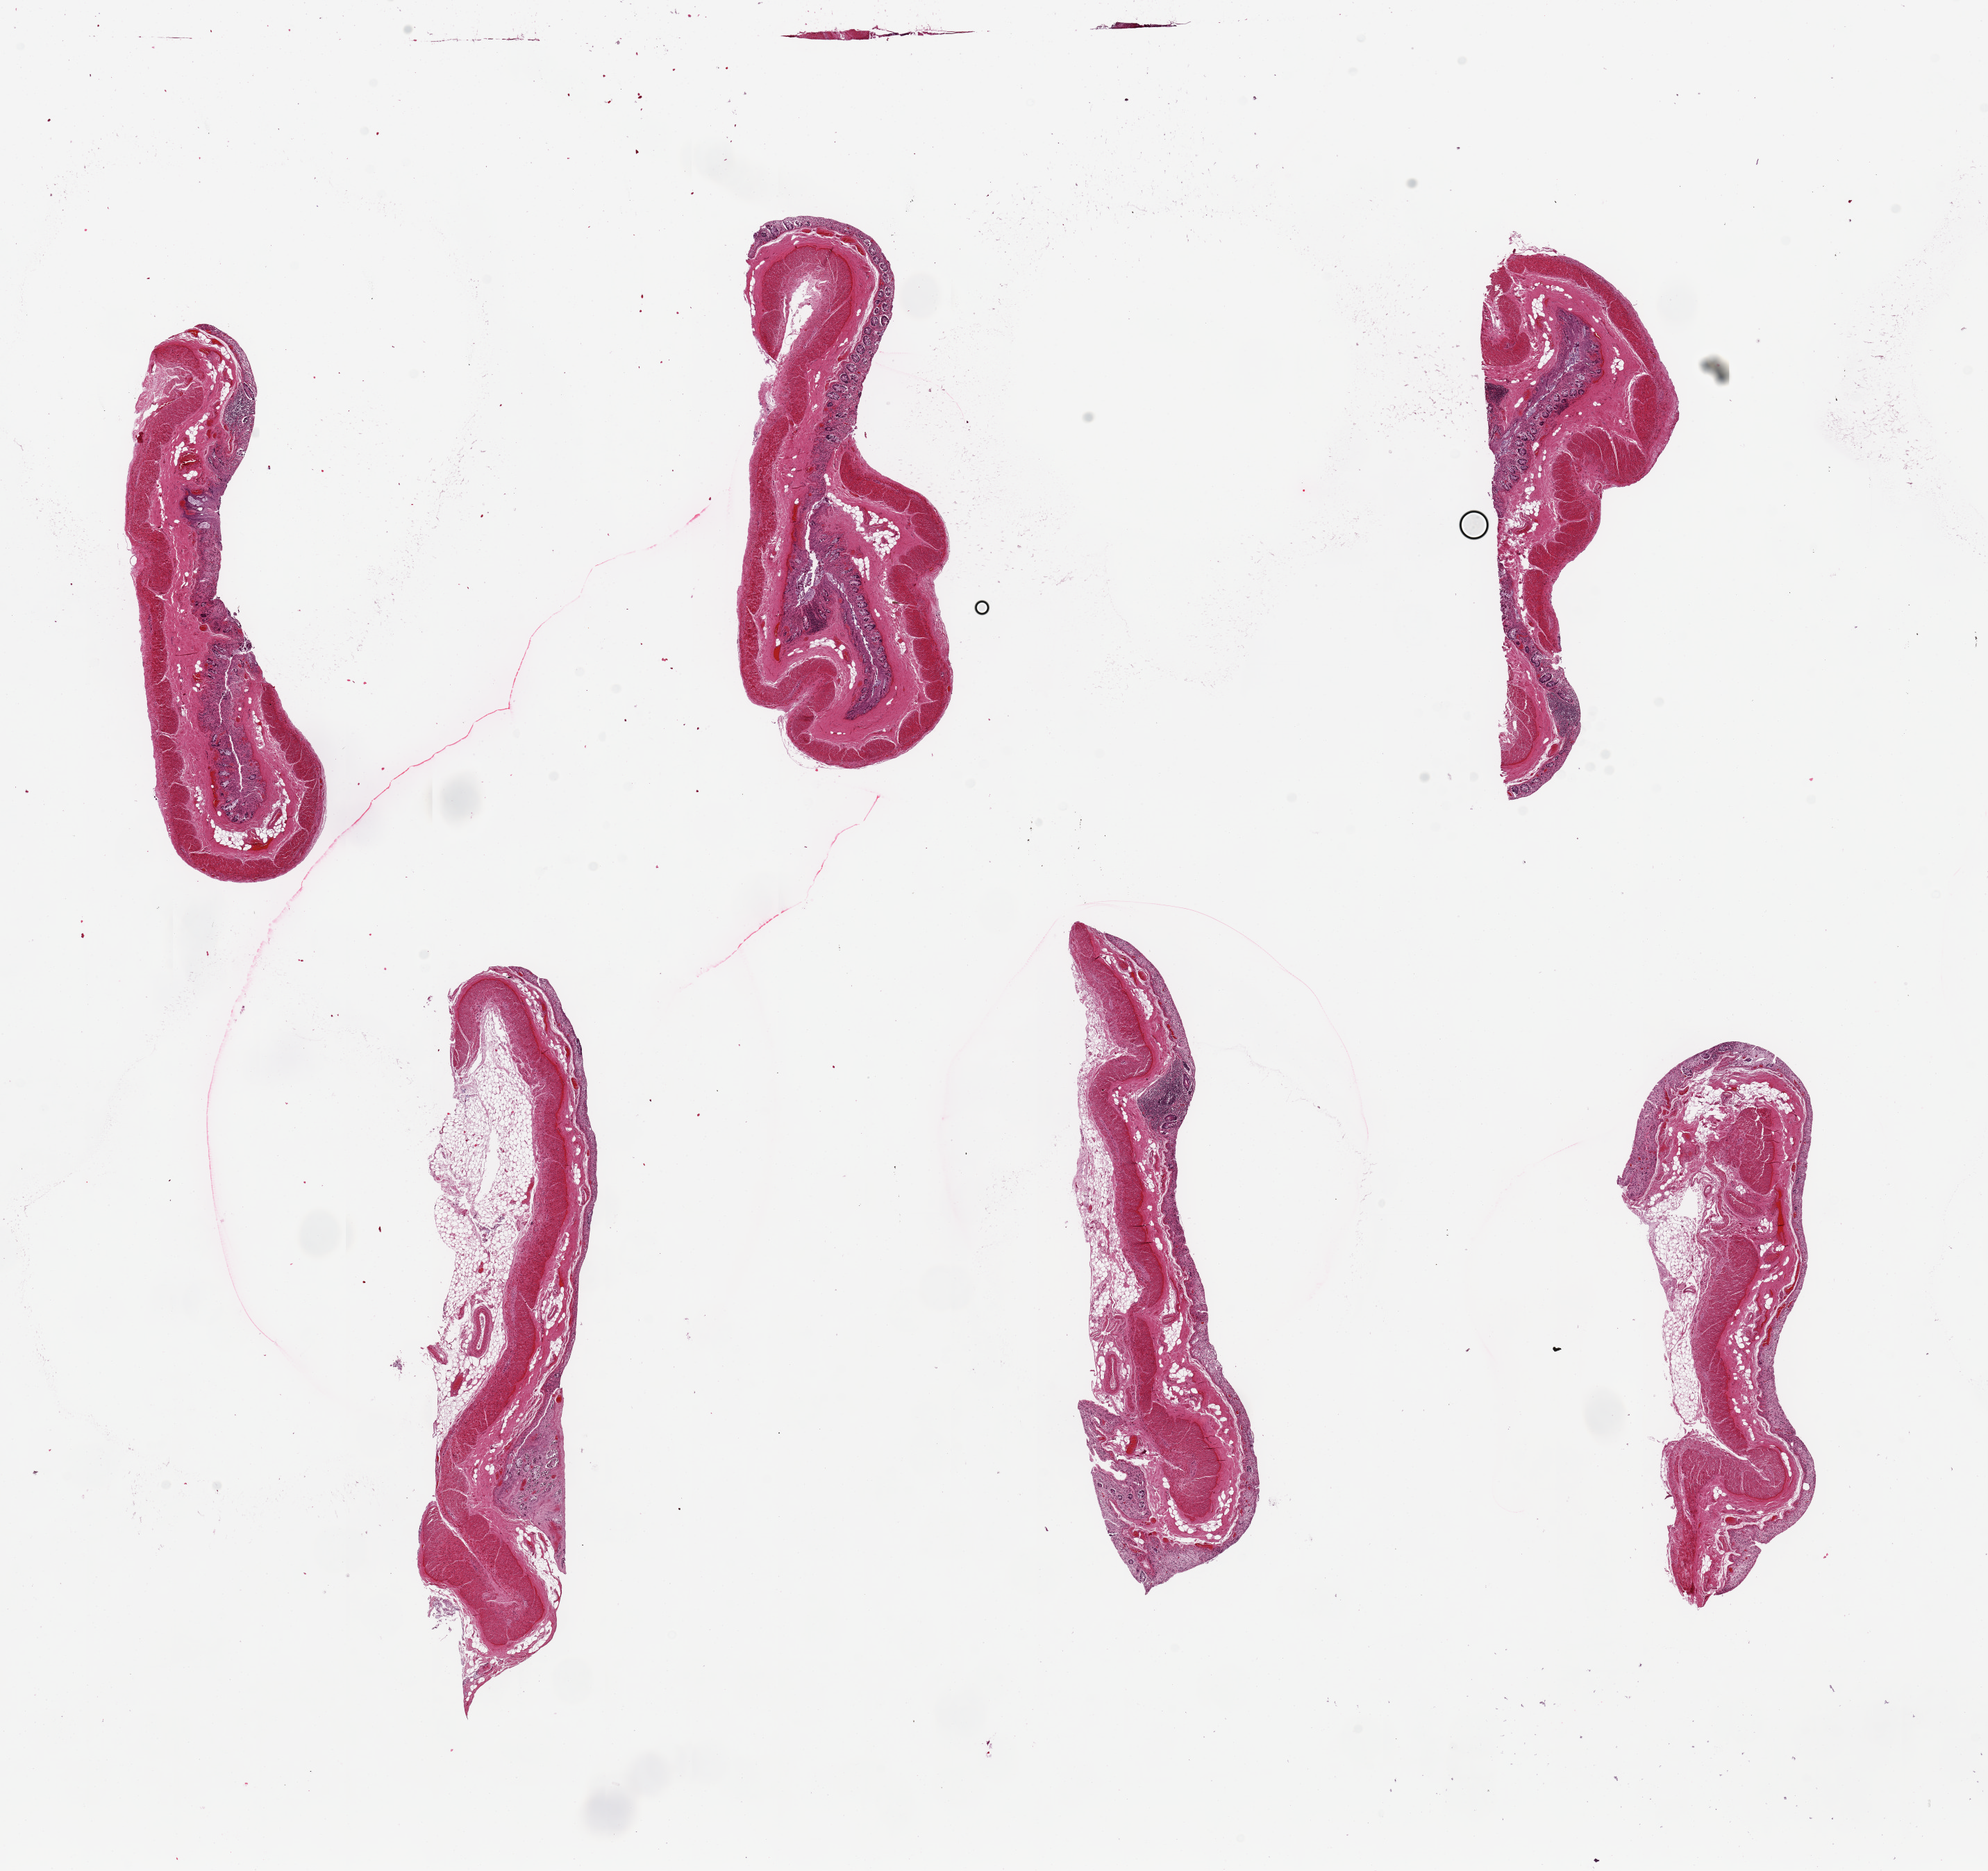
Digitized hematoxylin and eosin (H&E)-stained section, a low-resolution overview of the entire scanned area, about 22.6 x 21.3 mm (from a 20x scan). PAXgene-fixed paraffin-embedded (PFPE) section. Sampled site (target tissue): transverse colon. Donor tissue sample. Donor sex: male.
Pathologist's review note for this sample: 6 pieces, up to 8.5x2mm; mucosa badly autolyzed, sloughed.